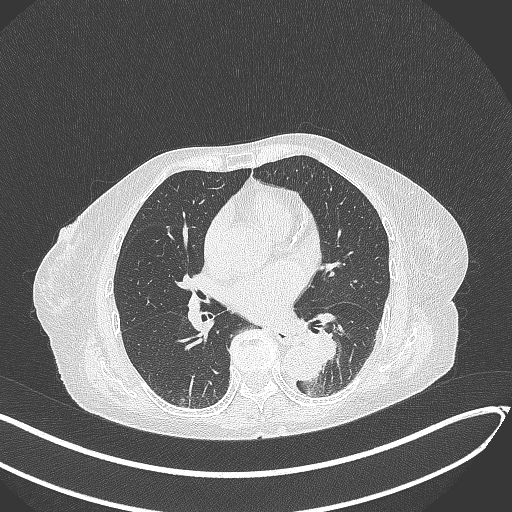
Chest CT, one axial slice; slice 120 of 324 in the series (ordered by position); reconstruction kernel B70f; lung window (W 1500 / L -600 HU); 1 mm slice thickness; 512 × 512 image matrix. Patient: female, 82 years. Case-level facts recorded for this patient, not image findings: clinical TNM (as recorded): T1b N0 M1.
Annotated regions visible in this slice (bounding box drawn by a radiologist):
- lung tumour (recorded histology: adenocarcinoma): bounding box <296,321,343,371> (left, top, right, bottom; pixels)